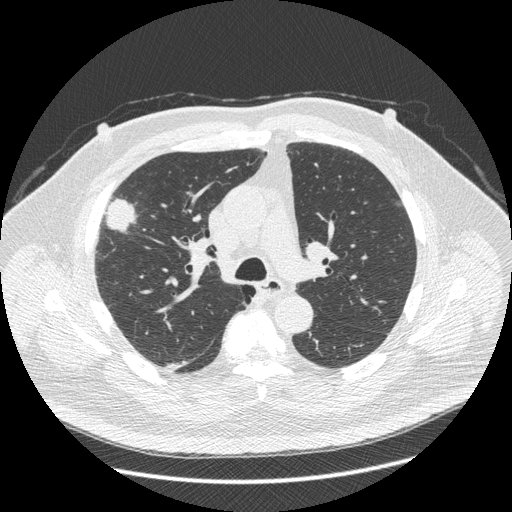
Low-dose screening chest CT, one axial slice; reconstruction kernel STANDARD; lung window (W 1500 / L -600 HU); 512 × 512 image matrix, field of view 400 × 400 mm.
Annotated regions visible in this slice (manually delineated by an expert):
- lesion 1 (tumor, upper lobe of right lung): box from (x=106, y=199) to (x=136, y=231) px